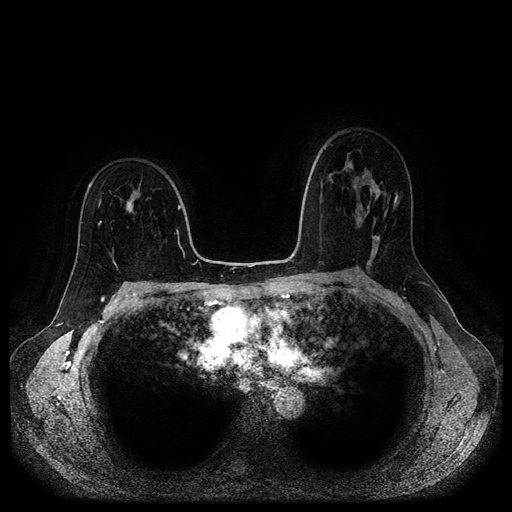
Breast MRI (dynamic contrast-enhanced, multi-phase), one axial slice. Position 65 of 116 along the scan axis. Dynamic contrast-enhanced series, time point 2 of 5 at this slice position (early post-contrast). 1.5 T. TE 2.6 ms, TR 5.3 ms. 2 mm slice thickness. 512 × 512 image matrix, field of view 360 × 360 mm. Female patient, age 50 years.
Annotated regions visible in this slice (semi-automatically segmented with operator editing):
- breast lesion (labelled benign in the annotation): box from (x=122, y=187) to (x=141, y=216) px